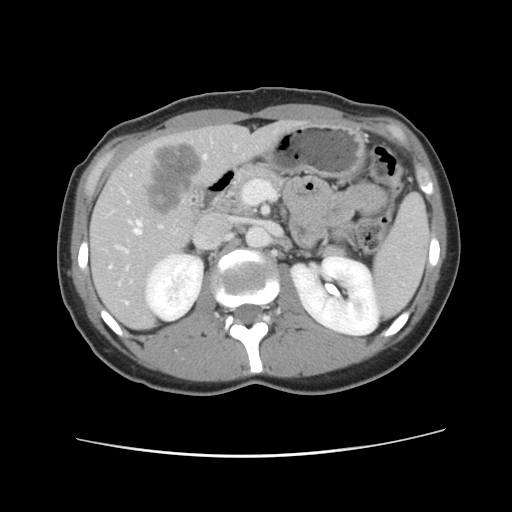
Contrast-enhanced abdominal CT, one axial slice; position 52 of 134 along the scan axis; 120 kVp; intravenous contrast given; soft-tissue window (W 400 / L 40 HU); 2.5 mm slice thickness; 512 × 512 image matrix, field of view 339 × 339 mm. Female patient, age 33 years. Case-level facts recorded for this patient, not image findings: diagnosis: colorectal cancer liver metastases, imaged before liver resection; multiple liver metastases: yes; largest metastasis: 4.5 cm; chemotherapy before resection: no.
Outlined on this slice (outlined manually by an expert reader):
- hepatic veins: box from (x=111, y=156) to (x=207, y=304) px
- liver: (x=91, y=122)–(x=300, y=329)
- planned liver remnant (the part of the liver to remain after resection): (x=91, y=122)–(x=299, y=329)
- liver metastasis: (x=142, y=141)–(x=201, y=217)